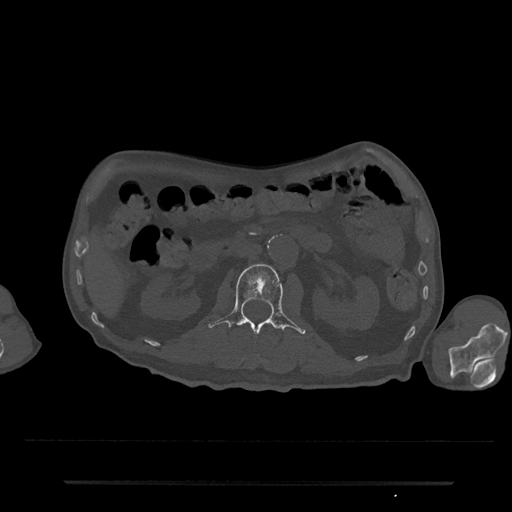
CT including the spine, one axial slice; position 71 of 797 along the scan axis; reconstruction kernel Br40s/3; bone window (W 1800 / L 400 HU); 512 × 512 image matrix, field of view 427 × 427 mm. Patient: male, 74 years. From the clinical record (not read from this slice): primary cancer: prostate.
Outlined on this slice (semi-automatic segmentation, software-assisted and operator-edited):
- L2 vertebra: bounding box (x1, y1, x2, y2) in pixels: (208, 264, 306, 334)